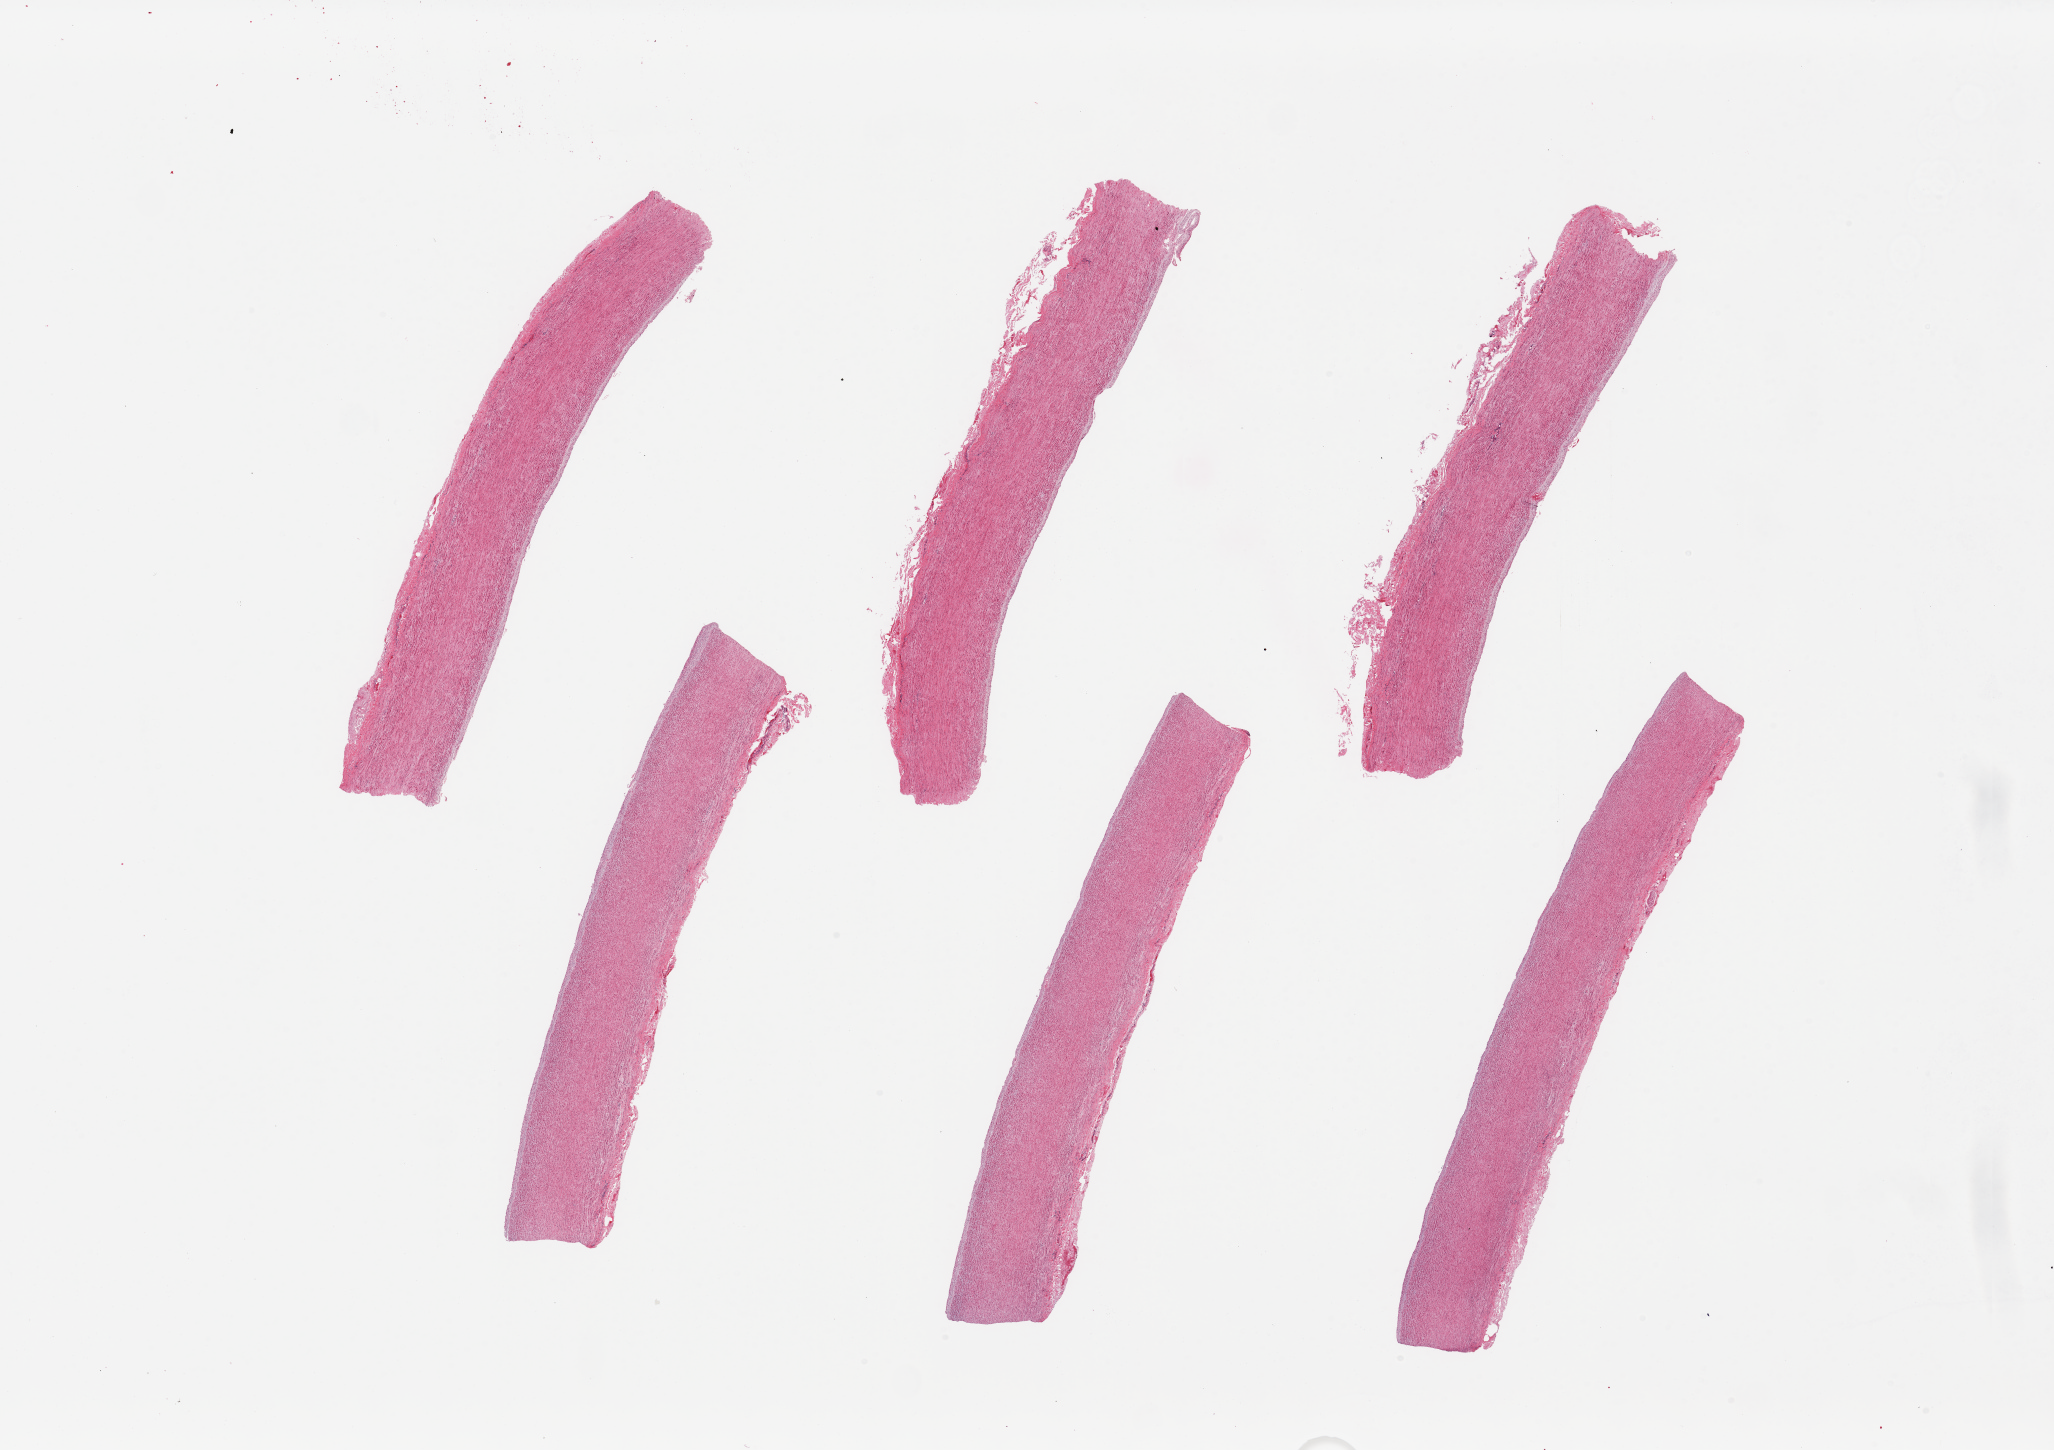
Digitized hematoxylin and eosin (H&E)-stained section, brightfield, whole scanned area (about 32.5 x 22.9 mm, from a 20x scan) shown as a low-resolution overview; PAXgene-fixed paraffin-embedded (PFPE) section; sampled site (target tissue): aorta; donor tissue sample. Donor: female.
Reviewer comment on this tissue sample: 6 pieces; intimal thickening.